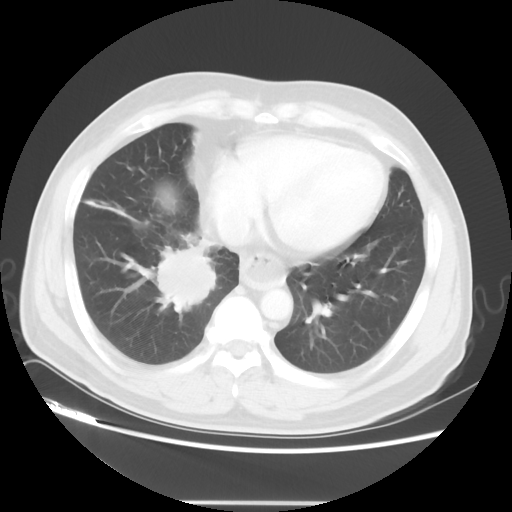
Chest CT, one axial slice; reconstruction kernel STANDARD; 120 kVp; lung window (W 1500 / L -600 HU); 5 mm slice thickness; 512 × 512 image matrix. Male patient, age 53 years. From the clinical record (not read from this slice): clinical TNM (as recorded): T2 N3 M0.
Outlined on this slice (bounding box drawn by a radiologist):
- lung tumour (recorded histology: small cell carcinoma): bounding box <157,236,224,317> (left, top, right, bottom; pixels)